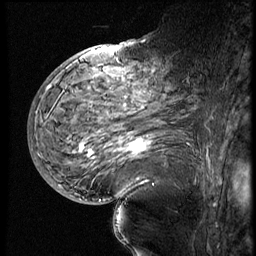
Breast MRI (dynamic contrast-enhanced), one sagittal slice; slice 33 of 60 in the series (ordered by position); 4 images stored at this slice position (order not interpretable as contrast timing); 1.5 T; TE 4.2 ms, TR 9 ms; 2.5 mm slice thickness; 256 × 256 image matrix, field of view 180 × 180 mm. Female patient, age 56 years. Case-level facts recorded for this patient, not image findings: setting: breast cancer imaged before/during neoadjuvant chemotherapy; receptor status: HER2-positive.
Outlined on this slice (semi-automatically segmented with operator editing):
- analysis volume of interest (the breast-tissue region the enhancement analysis was run in; not a lesion): bounding box [x1, y1, x2, y2] px = [82, 83, 199, 177]
- tumour enhancement mask (voxels above the 140 % enhancement threshold inside the analysis volume of interest): [120, 139, 153, 154]